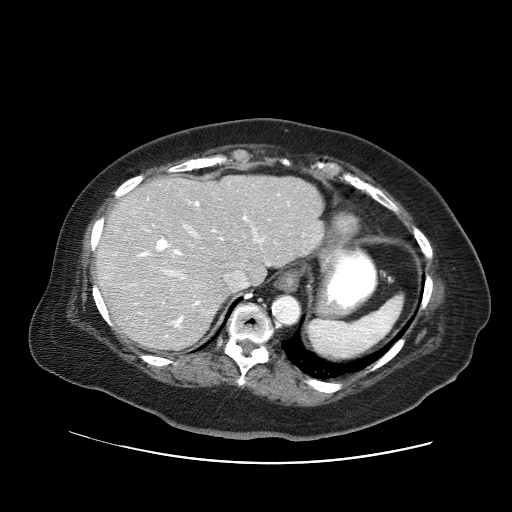
Contrast-enhanced abdominal CT (liver protocol), one axial slice; position 45 of 71 along the scan axis; 120 kVp; soft-tissue window (W 400 / L 40 HU); 512 × 512 image matrix. From the clinical record (not read from this slice): diagnosis: hepatocellular carcinoma (patient treated with transarterial chemoembolisation; whether this scan precedes or follows treatment is not stated here); TNM stage (as recorded): Stage-II; Child-Pugh class: A.
Annotated regions visible in this slice (semi-automatically segmented with operator editing):
- liver parenchyma outside the tumour (the mass and vessels are separate outlines, so this box may not span the whole liver): box from (x=94, y=176) to (x=324, y=350) px
- liver vessels: (x=105, y=198)–(x=269, y=338)